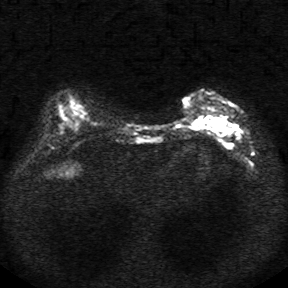
Breast MRI, one axial slice; slice 10 of 34 in the series (ordered by position); diffusion-weighted series; image 2 of 4 stored at this slice position (different b-values; order by instance number); 1.5 T; 5 mm slice thickness; 288 × 288 image matrix, field of view 340 × 340 mm. Female patient.
Annotated regions visible in this slice (expert manual segmentation):
- tumour on diffusion-weighted imaging: bounding box <191,116,238,134> (left, top, right, bottom; pixels)